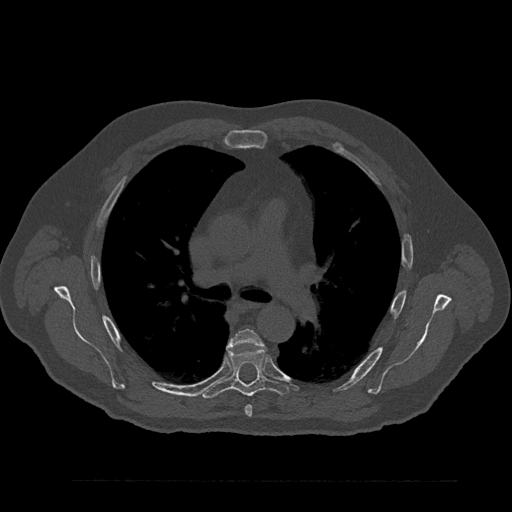
CT including the spine, one axial slice. Reconstruction kernel Br40s/3. Bone window (W 1800 / L 400 HU). 0.5 mm slice thickness. 512 × 512 image matrix. Patient: male, 61 years. Case-level facts recorded for this patient, not image findings: primary cancer: prostate.
Annotated regions visible in this slice (semi-automatic segmentation, software-assisted and operator-edited):
- T5 vertebra: bounding box <229,328,263,417> (left, top, right, bottom; pixels)
- T6 vertebra: <201,348,288,399>